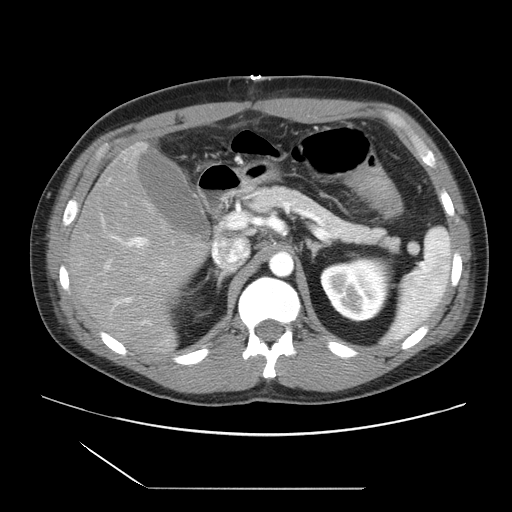
Contrast-enhanced abdominal CT, one axial slice. Position 14 of 39 along the scan axis. Intravenous contrast given. Soft-tissue window (W 400 / L 40 HU). 5 mm slice thickness. 512 × 512 image matrix, field of view 395 × 395 mm. Male patient, age 39 years. Case-level facts recorded for this patient, not image findings: diagnosis: colorectal cancer liver metastases, imaged before liver resection; multiple liver metastases: yes; largest metastasis: 1.3 cm; disease in both lobes: no.
Outlined on this slice (expert manual segmentation):
- hepatic veins: bounding box [x1, y1, x2, y2] px = [217, 239, 249, 269]
- liver: [67, 146, 209, 355]
- planned liver remnant (the part of the liver to remain after resection): [131, 146, 142, 158]
- portal vein (with intrahepatic branches): [104, 212, 240, 325]